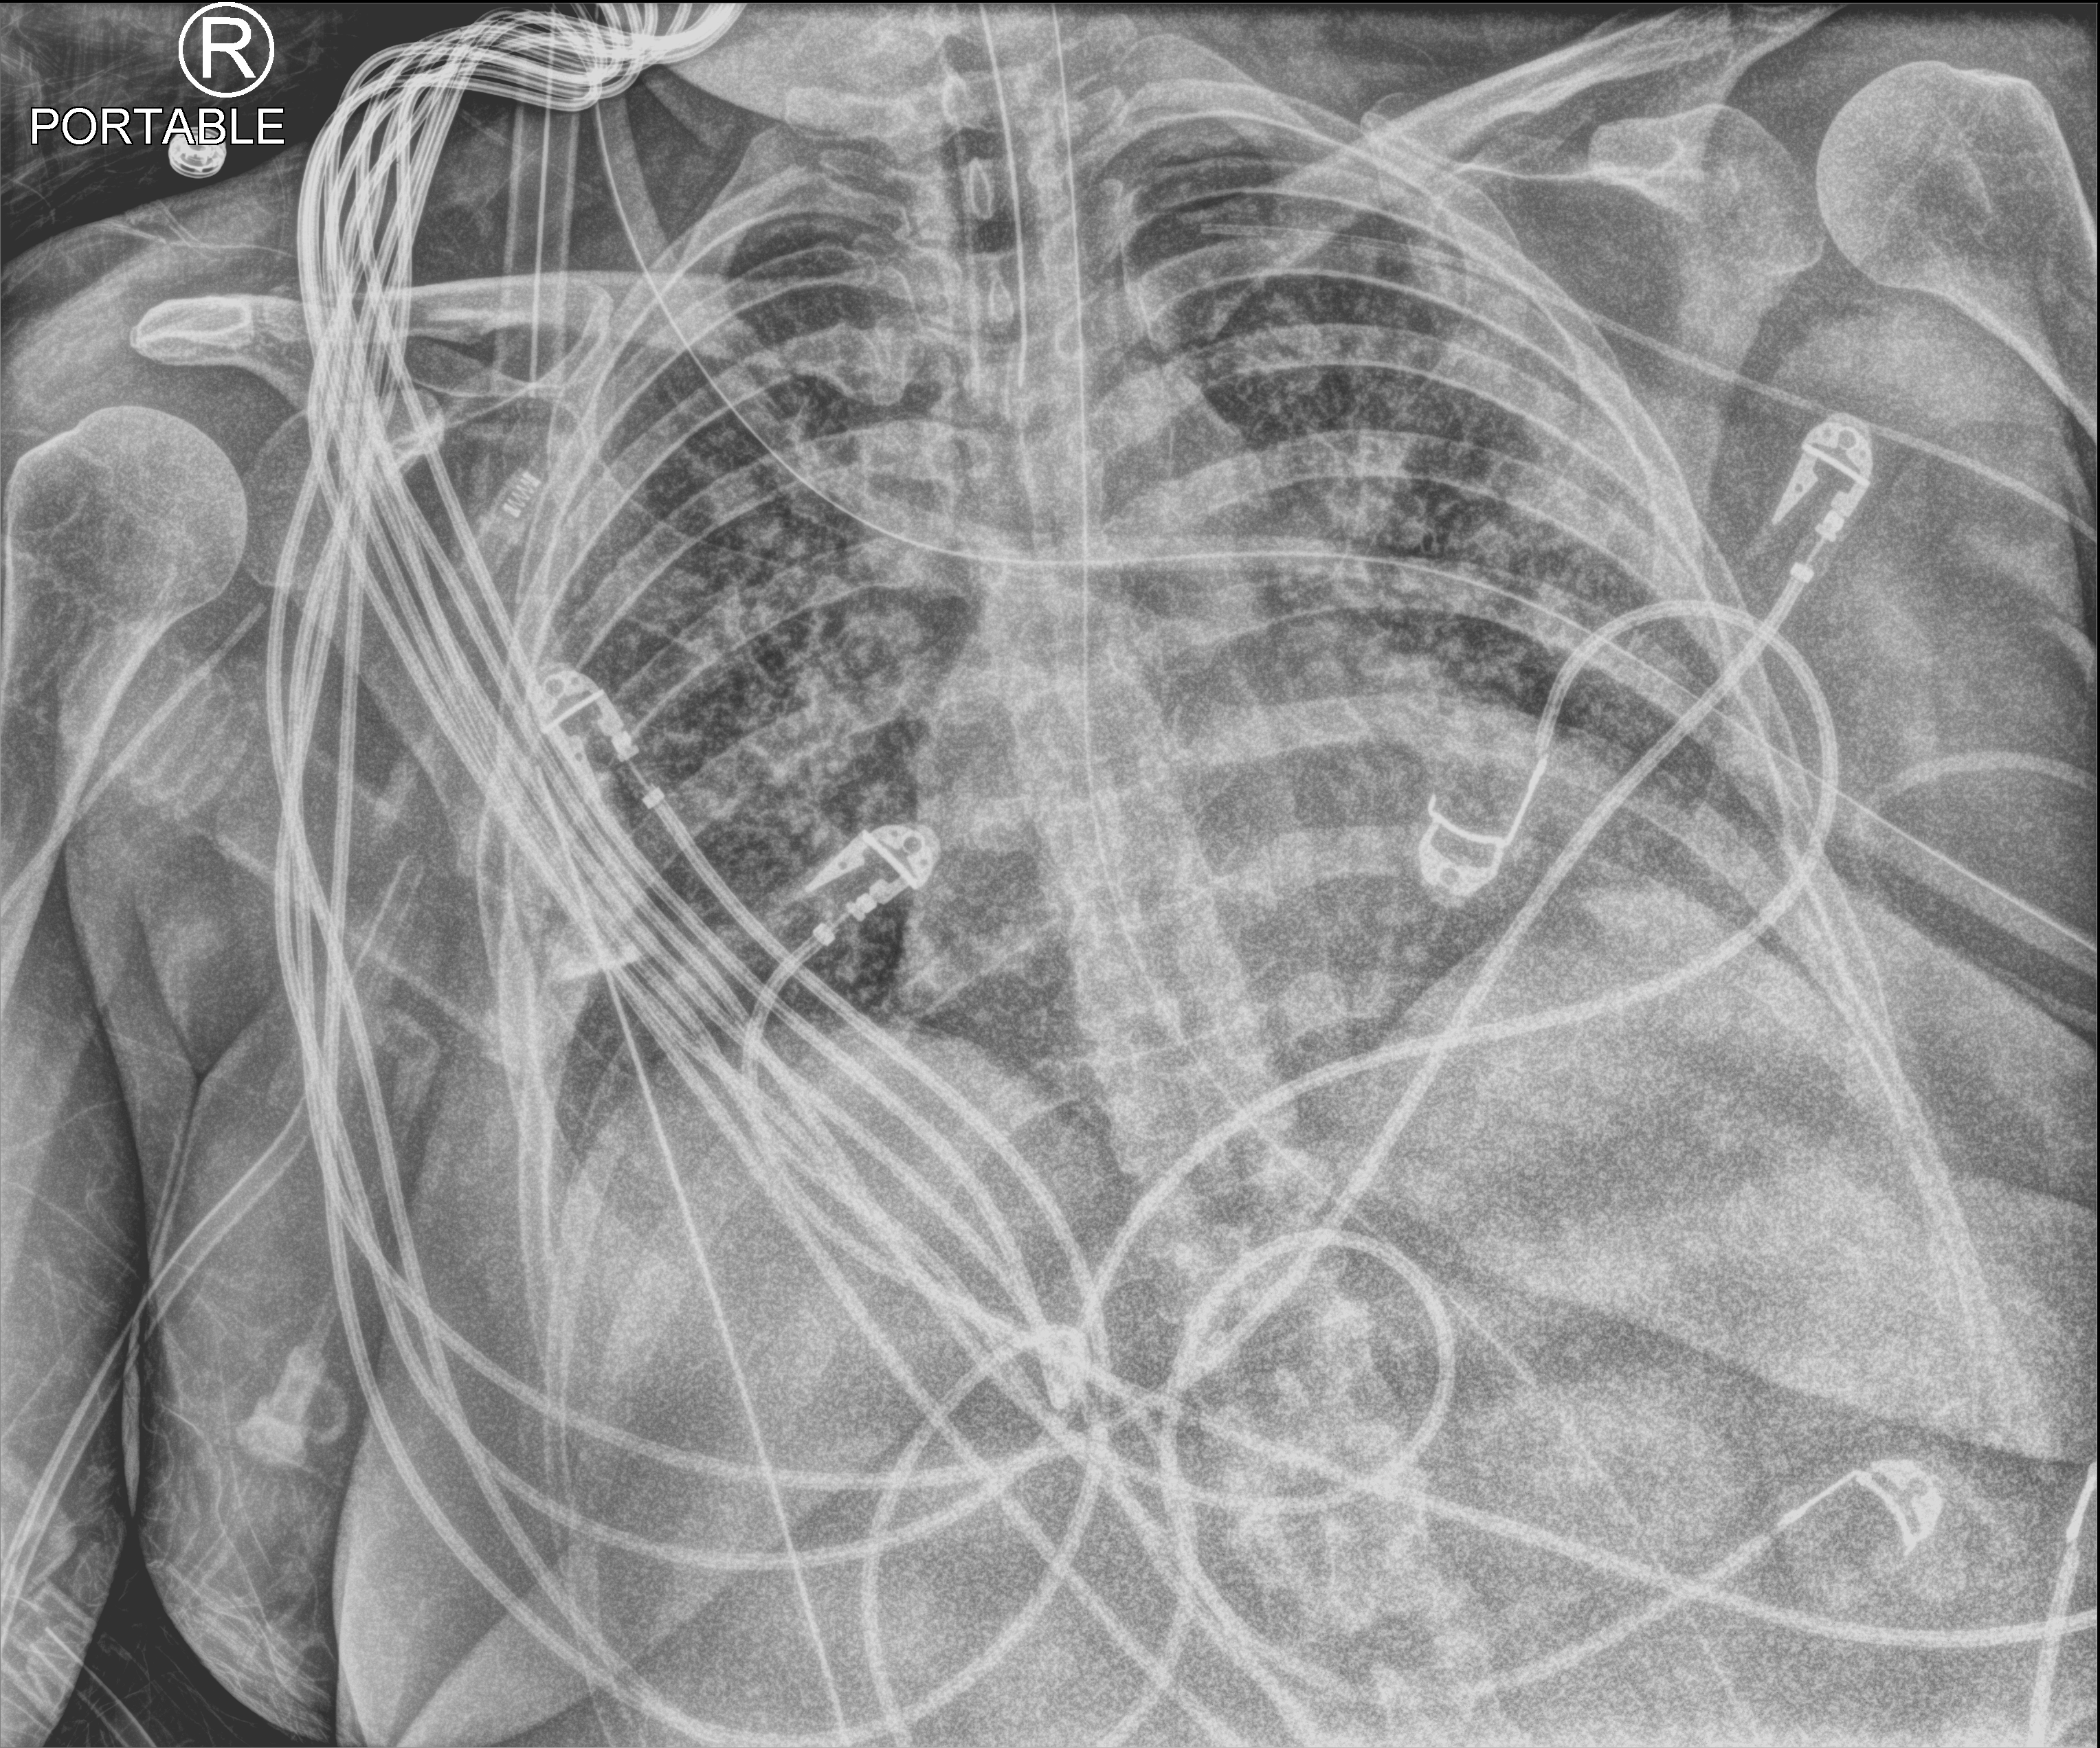
Portable chest radiograph, anteroposterior (AP) projection. Female patient hospitalised with COVID-19, age 18–59 years.
Hospital-stay facts (about this admission, not read from this image; timing relative to this image not recorded): smoking status (admission record): never.